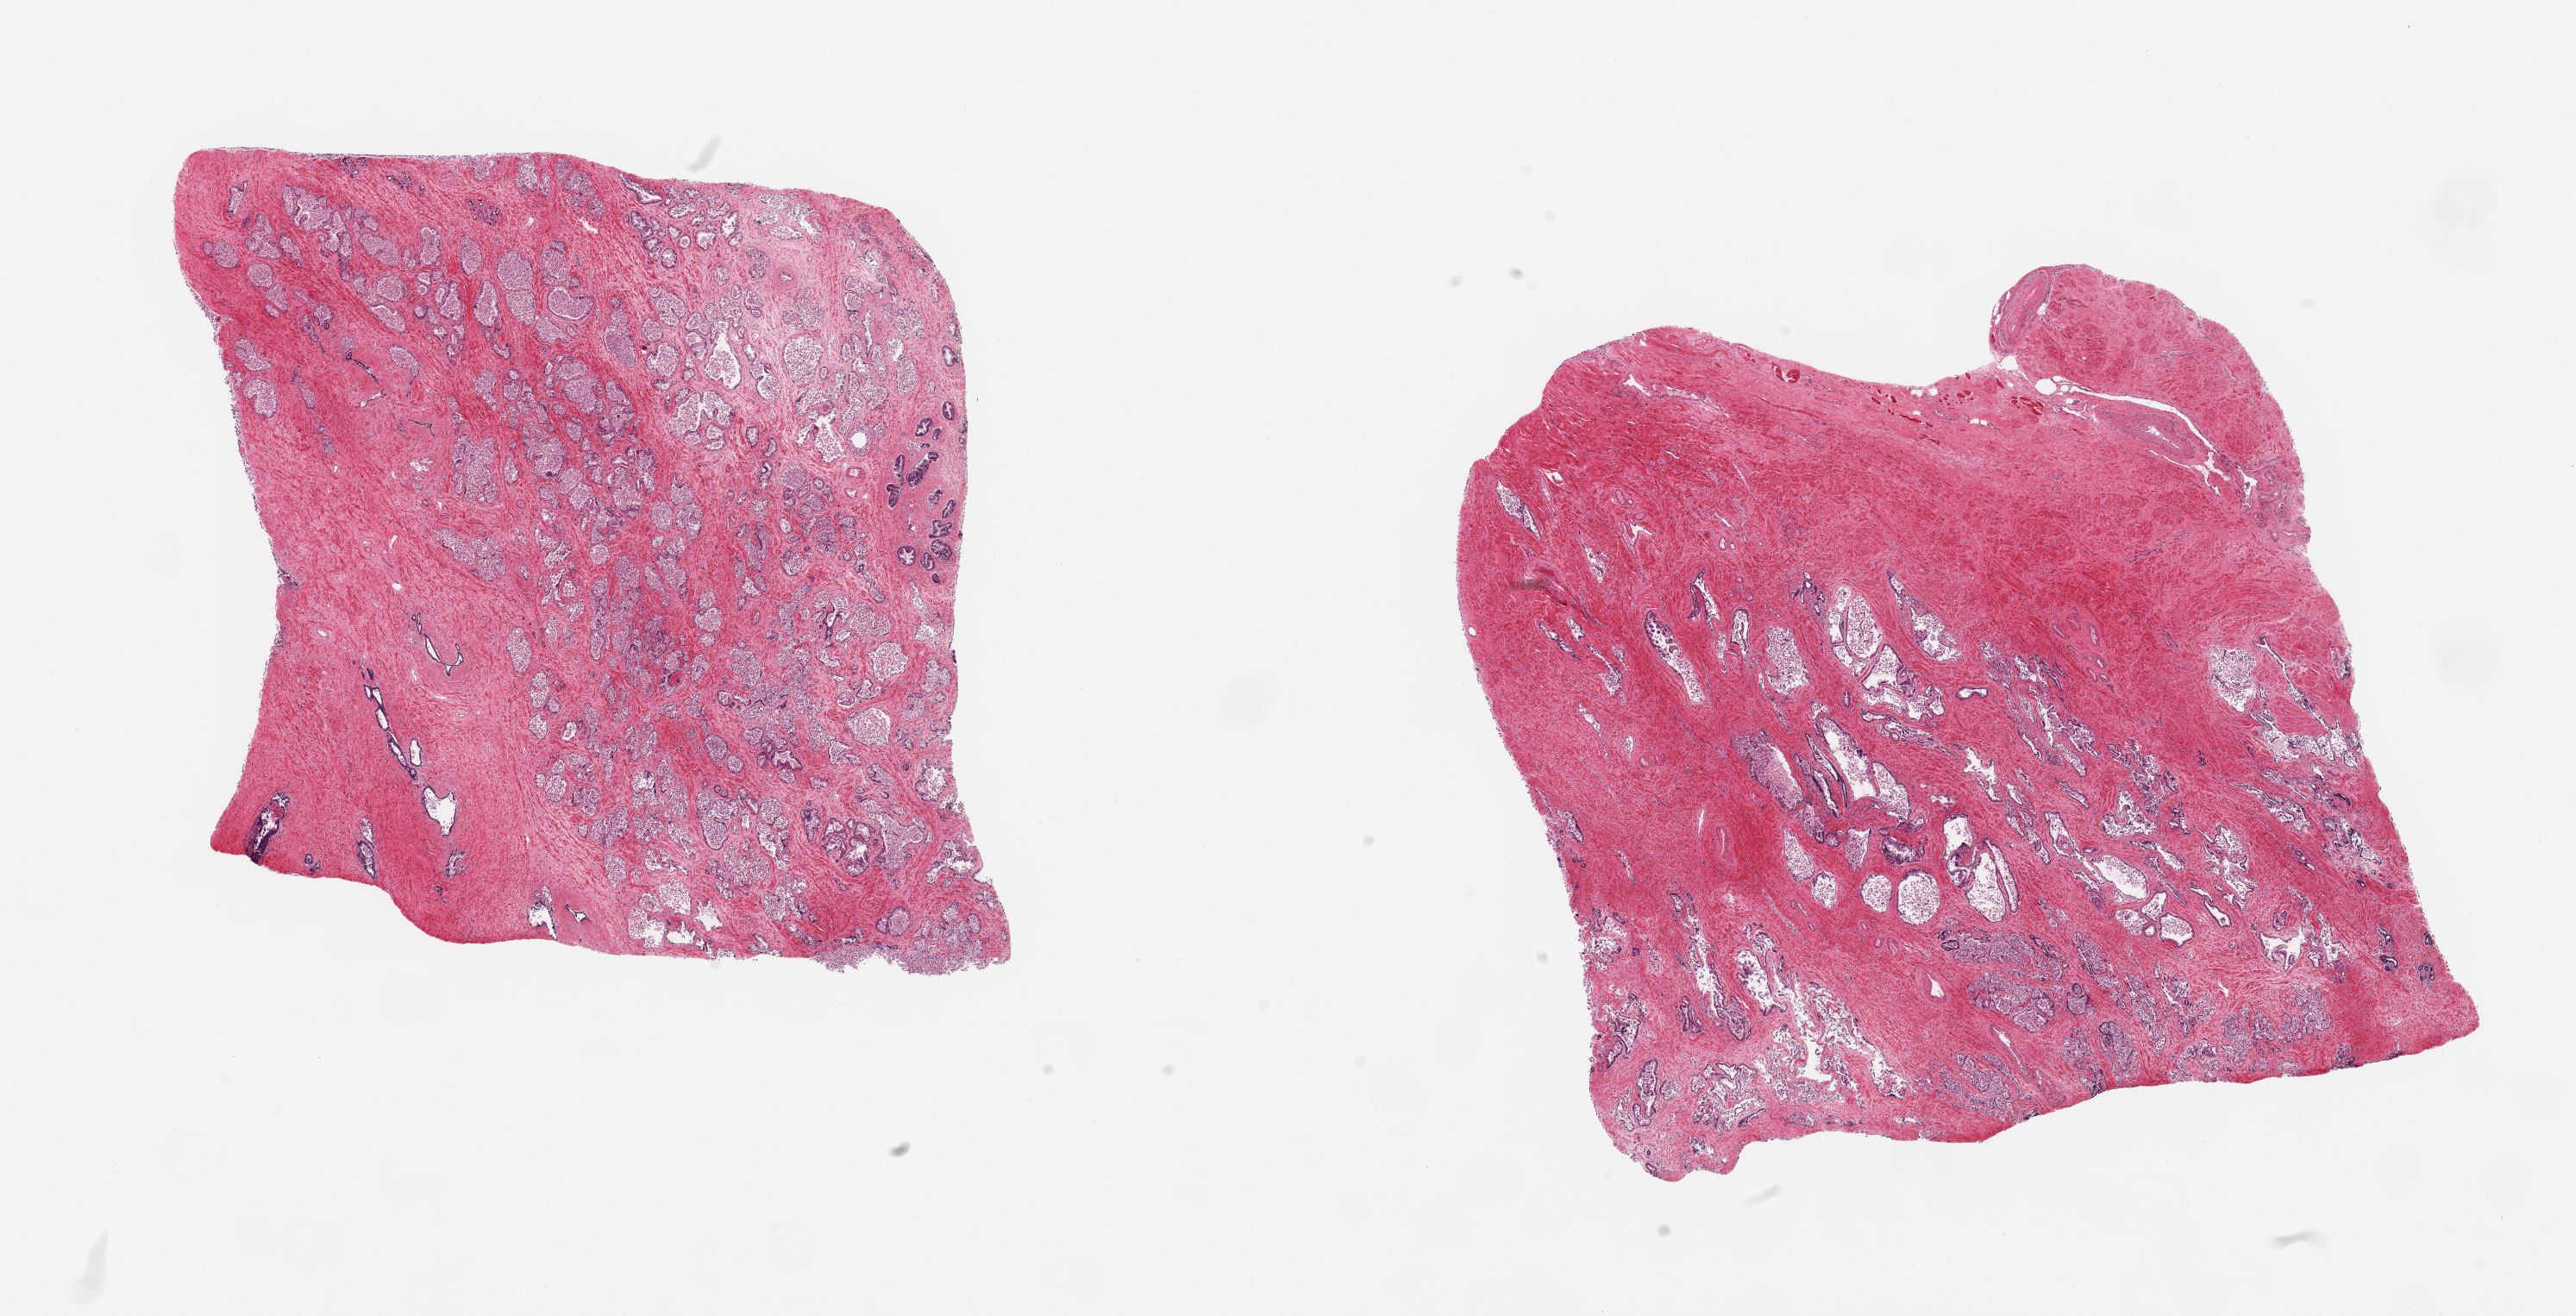
Digitized H&E-stained section, brightfield, a low-resolution overview of the entire scanned area, about 23.6 x 12.1 mm (from a 20x scan). PAXgene-fixed, paraffin-embedded tissue. Sampled site (target tissue): prostate. Donor tissue sample. Donor sex: male.
Pathologist's review note for this sample: 2 pieces, glandular elements with moderately/markedly advanced autolysis.